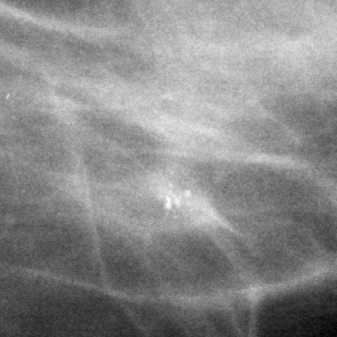
Region of interest cut from a scanned film mammogram (one marked finding); left breast; MLO view.
- Finding: calcifications, morphology pleomorphic, distribution clustered; BI-RADS assessment category 3; subtlety rating 3 on a 1 (subtle) to 5 (obvious) scale; pathology (as recorded): benign.